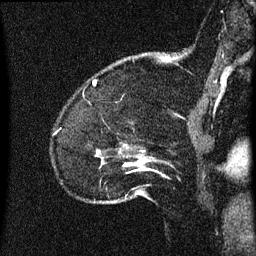
Breast MRI (dynamic contrast-enhanced), one sagittal slice. Position 10 of 60 along the scan axis. Dynamic contrast-enhanced series, image 2 of 3 at this slice position (ordered by acquisition). 1.5 T. TE 4.2 ms, TR 8 ms. 2 mm slice thickness. 256 × 256 image matrix, field of view 180 × 180 mm. Female patient, age 52 years.
Outlined on this slice (semi-automatic segmentation, software-assisted and operator-edited):
- analysis volume of interest (the breast-tissue region the enhancement analysis was run in; not a lesion): box from (x=95, y=144) to (x=151, y=203) px
- tumour enhancement mask (voxels above the 70 % enhancement threshold inside the analysis volume of interest): (x=97, y=150)–(x=147, y=171)